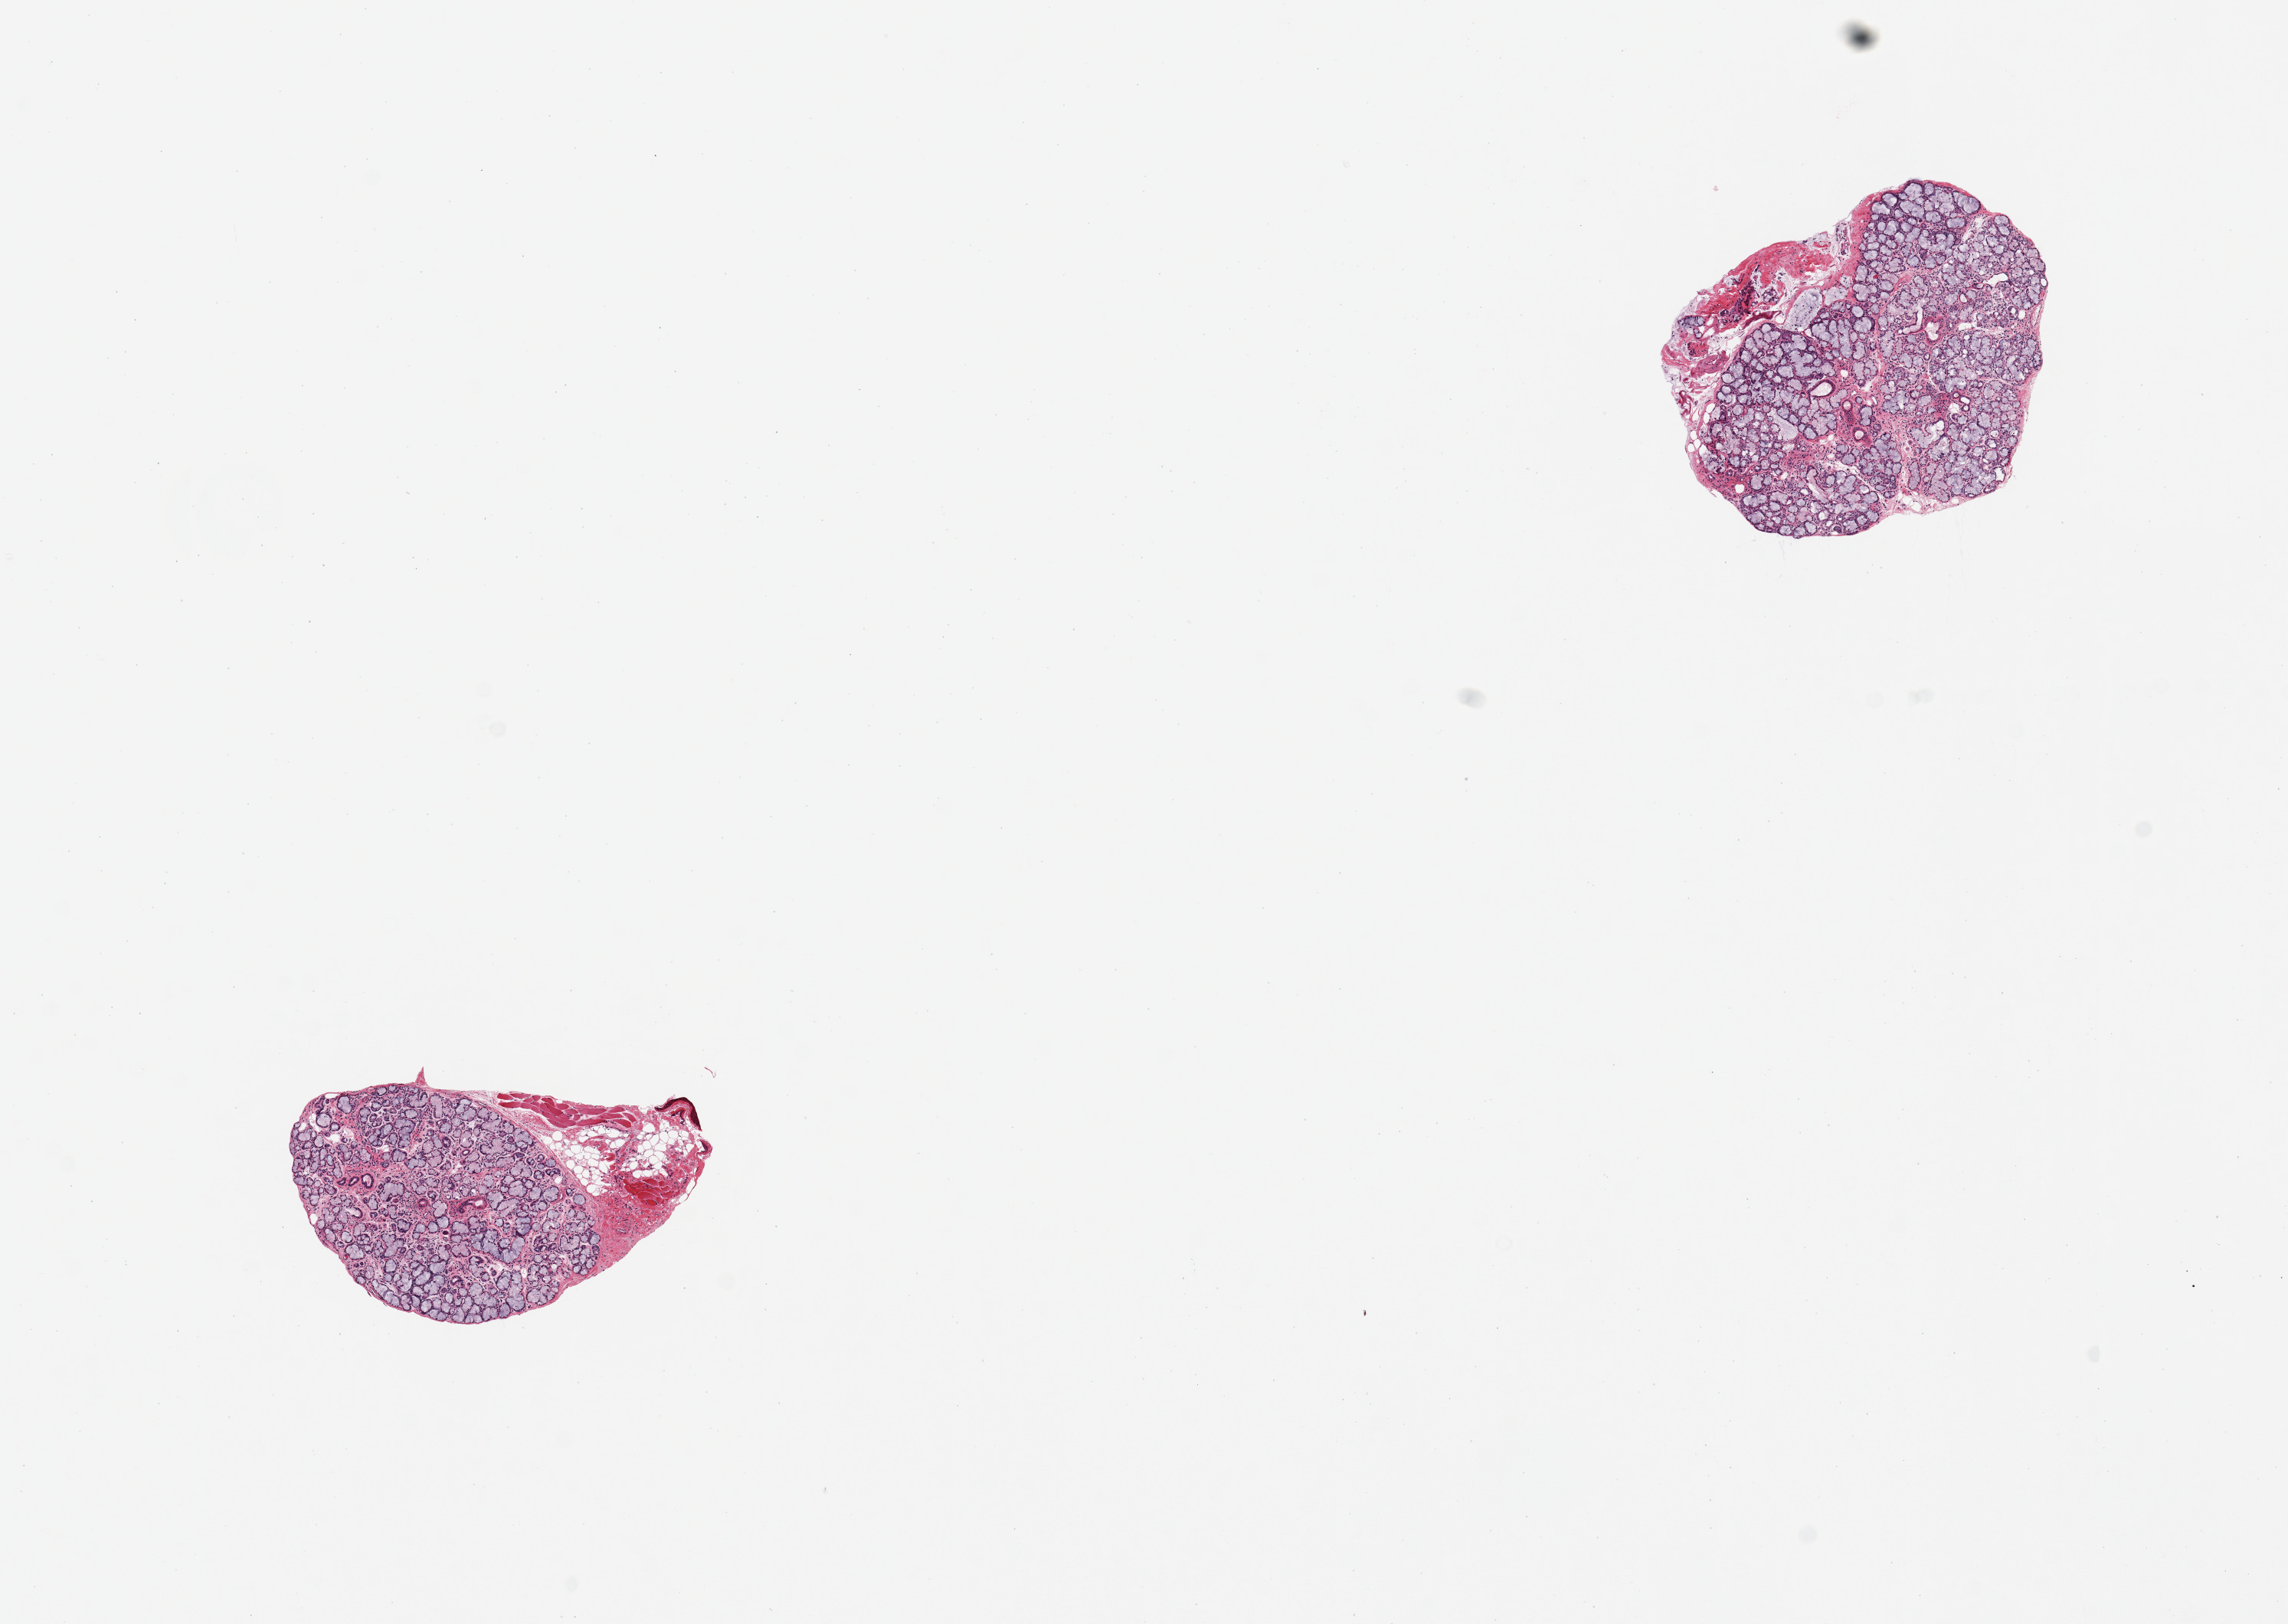
Whole-slide image, haematoxylin and eosin stain, a low-resolution overview of the entire scanned area, about 11.8 x 8.4 mm (from a 20x scan); PAXgene-fixed, paraffin-embedded tissue; sampled site (target tissue): minor salivary gland; donor tissue sample. Donor: male.
* review note (as recorded): 2 pieces; excellent specimen, one piece does include 20% attachment of lip and skeletal muscle